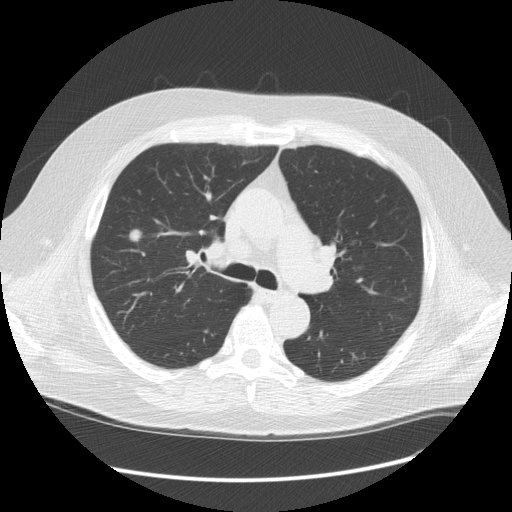
Low-dose screening chest CT, axial slice; third annual screen; lung window (W 1500 / L -600 HU); 2.5 mm slice thickness; standard (soft-tissue) reconstruction kernel (STANDARD); slice 45 of 128 in the series. Male, age 61 years at enrolment.
• Lesion marked by an expert reader, bounding box <110,217,152,256> (left, top, right, bottom; pixels).
• Screening reader's record for this exam (one nodule recorded; not confirmed to be the boxed lesion): non-calcified nodule or mass ≥4 mm, right upper lobe, 13 × 11 mm, spiculated (stellate) margins, soft tissue attenuation, pre-existing on the prior screen: yes; interval growth: yes.
• Official screen result: positive, other.
• Later outcome: lung cancer diagnosed 21 days after this screen — adenocarcinoma, NOS, right upper lobe, stage IIIA (AJCC 6th edition), 13 mm at pathology.